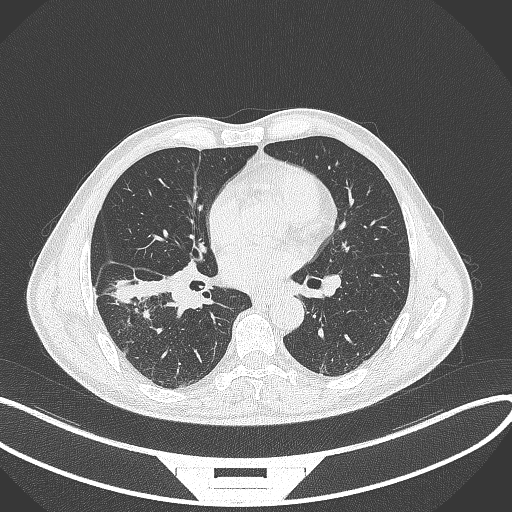
Chest CT, one axial slice. Position 172 of 364 along the scan axis. Lung window (W 1500 / L -600 HU). 512 × 512 image matrix. Male patient, age 58 years. Case-level facts recorded for this patient, not image findings: clinical TNM (as recorded): T3 N0 M0.
Outlined on this slice (bounding box drawn by a radiologist):
- lung tumour (recorded histology: squamous cell carcinoma): bounding box <112,274,168,307> (left, top, right, bottom; pixels)